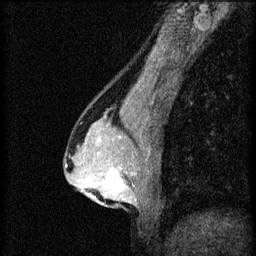
Breast MRI (dynamic contrast-enhanced), one sagittal slice. Position 35 of 60 along the scan axis. 3 images stored at this slice position (order not interpretable as contrast timing). 1.5 T. TE 4.2 ms, TR 8.2 ms. 2 mm slice thickness. 256 × 256 image matrix, field of view 180 × 180 mm. Female patient, age 44 years.
Annotated regions visible in this slice (semi-automatically segmented with operator editing):
- analysis volume of interest (the breast-tissue region the enhancement analysis was run in; not a lesion): box from (x=94, y=162) to (x=143, y=205) px
- tumour enhancement mask (voxels above the 70 % enhancement threshold inside the analysis volume of interest): (x=94, y=170)–(x=125, y=199)